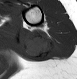
MRI of an extremity soft-tissue mass, one axial slice; position 9 of 28 along the scan axis; MR volume resampled by the dataset authors to the PET/CT grid (not the native acquisition matrix); 3.27 mm slice thickness; 77 × 79 image matrix, field of view 75 × 77 mm. Female patient. From the clinical record (not read from this slice): histological type: malignant fibrous histiocytoma; grade: low; site of the primary tumour: left arm.
Structures marked on this image (expert contour drawn on MRI and transferred to this co-registered scan by the dataset authors):
- gross tumour volume (mass): bounding box (x1, y1, x2, y2) in pixels: (24, 29, 56, 60)